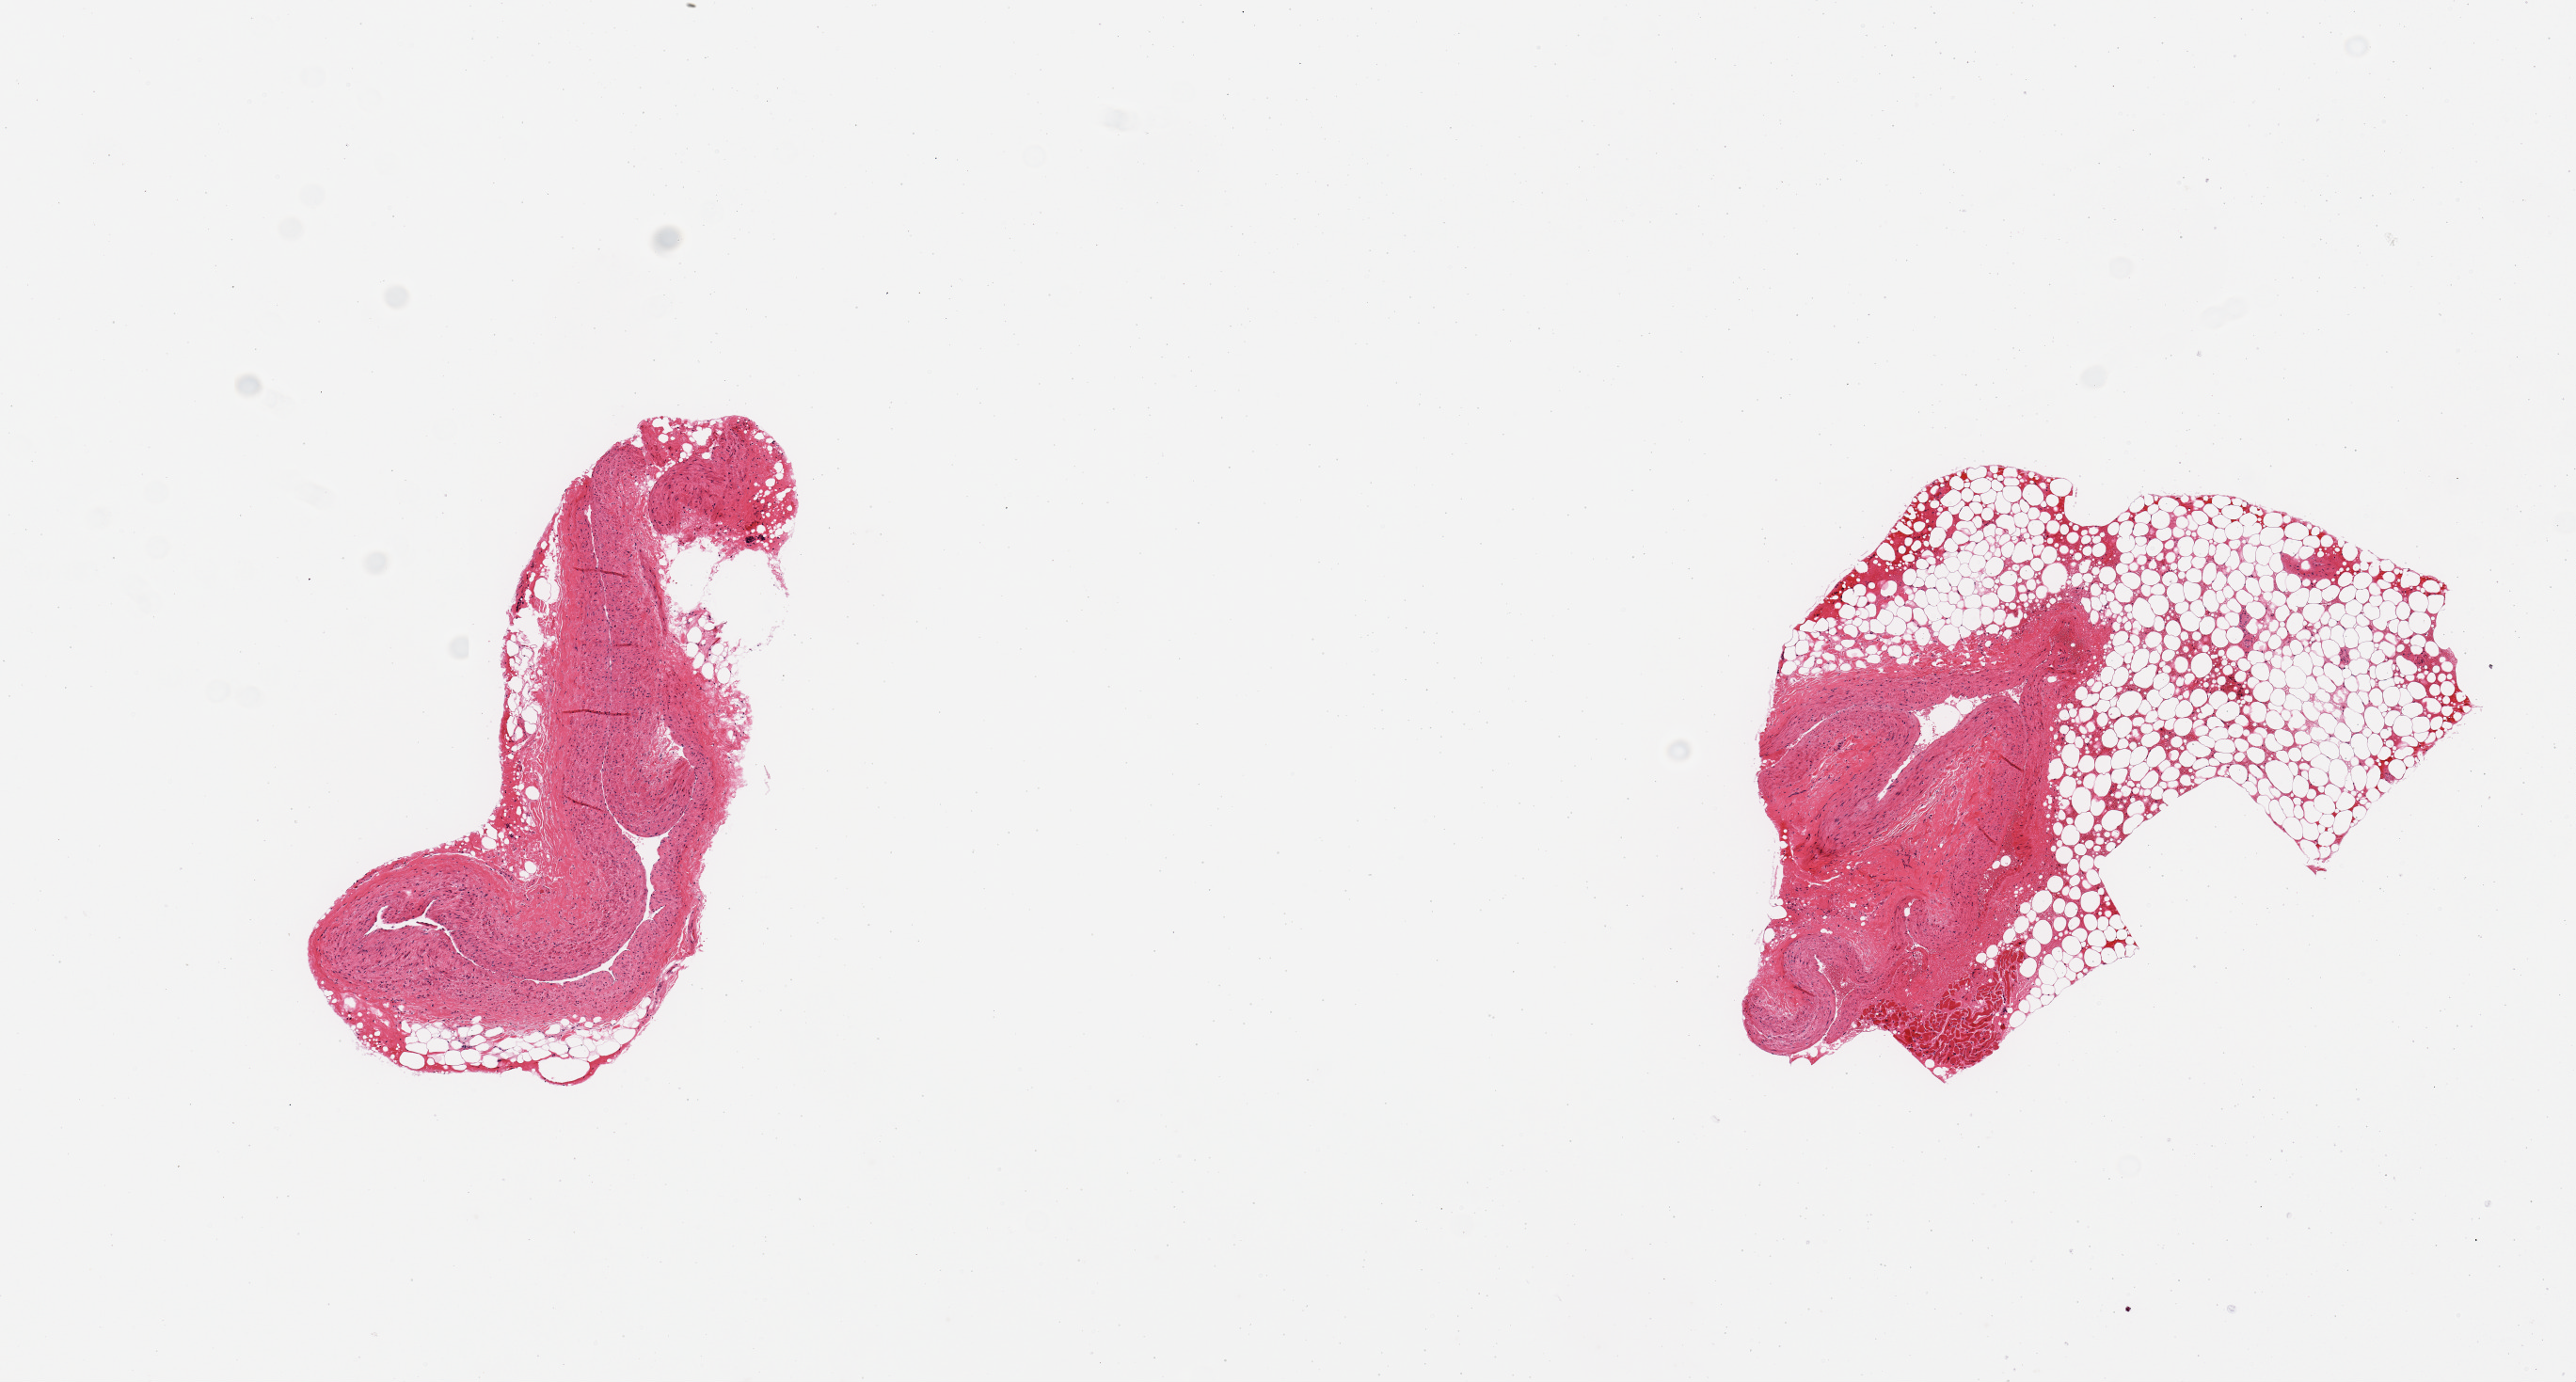
Digitized hematoxylin and eosin (H&E)-stained section, low-resolution overview of the scanned area, about 10.8 x 5.8 mm (slide scanned at 20x). PAXgene-fixed paraffin-embedded (PFPE) section. Section of coronary artery (target tissue). Tissue donor sample. Donor: male.
* pathologist's review note for this sample: 2 pieces, one includes 50% fat and cardiac muscle